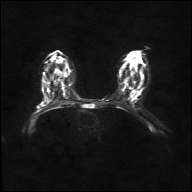
Breast MRI, one axial slice. Position 20 of 36 along the scan axis. Diffusion-weighted series; image 2 of 4 stored at this slice position (different b-values; order by instance number). 1.5 T. 4 mm slice thickness. 192 × 192 image matrix, field of view 360 × 360 mm. Female patient.
Structures marked on this image (outlined manually by an expert reader):
- tumour on diffusion-weighted imaging: bounding box (x1, y1, x2, y2) in pixels: (39, 104, 41, 107)